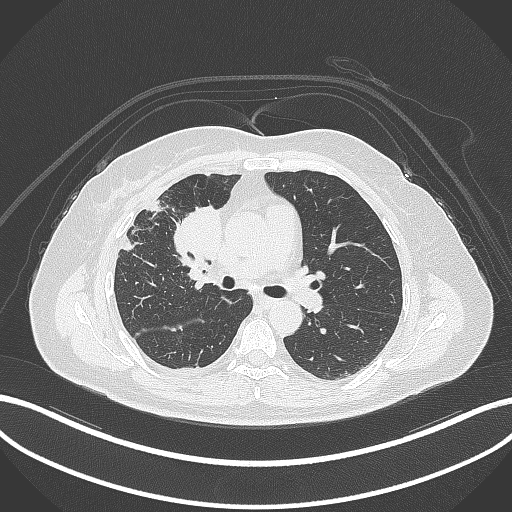
Chest CT, one axial slice. Position 165 of 305 along the scan axis. Reconstruction kernel B70f. 120 kVp. Lung window (W 1500 / L -600 HU). 512 × 512 image matrix, field of view 400 × 400 mm. Female patient, age 52 years. From the clinical record (not read from this slice): clinical TNM (as recorded): T3 N1 M1.
Outlined on this slice (rectangle marked by the reading radiologist):
- lung tumour (recorded histology: adenocarcinoma): box from (x=169, y=199) to (x=225, y=264) px